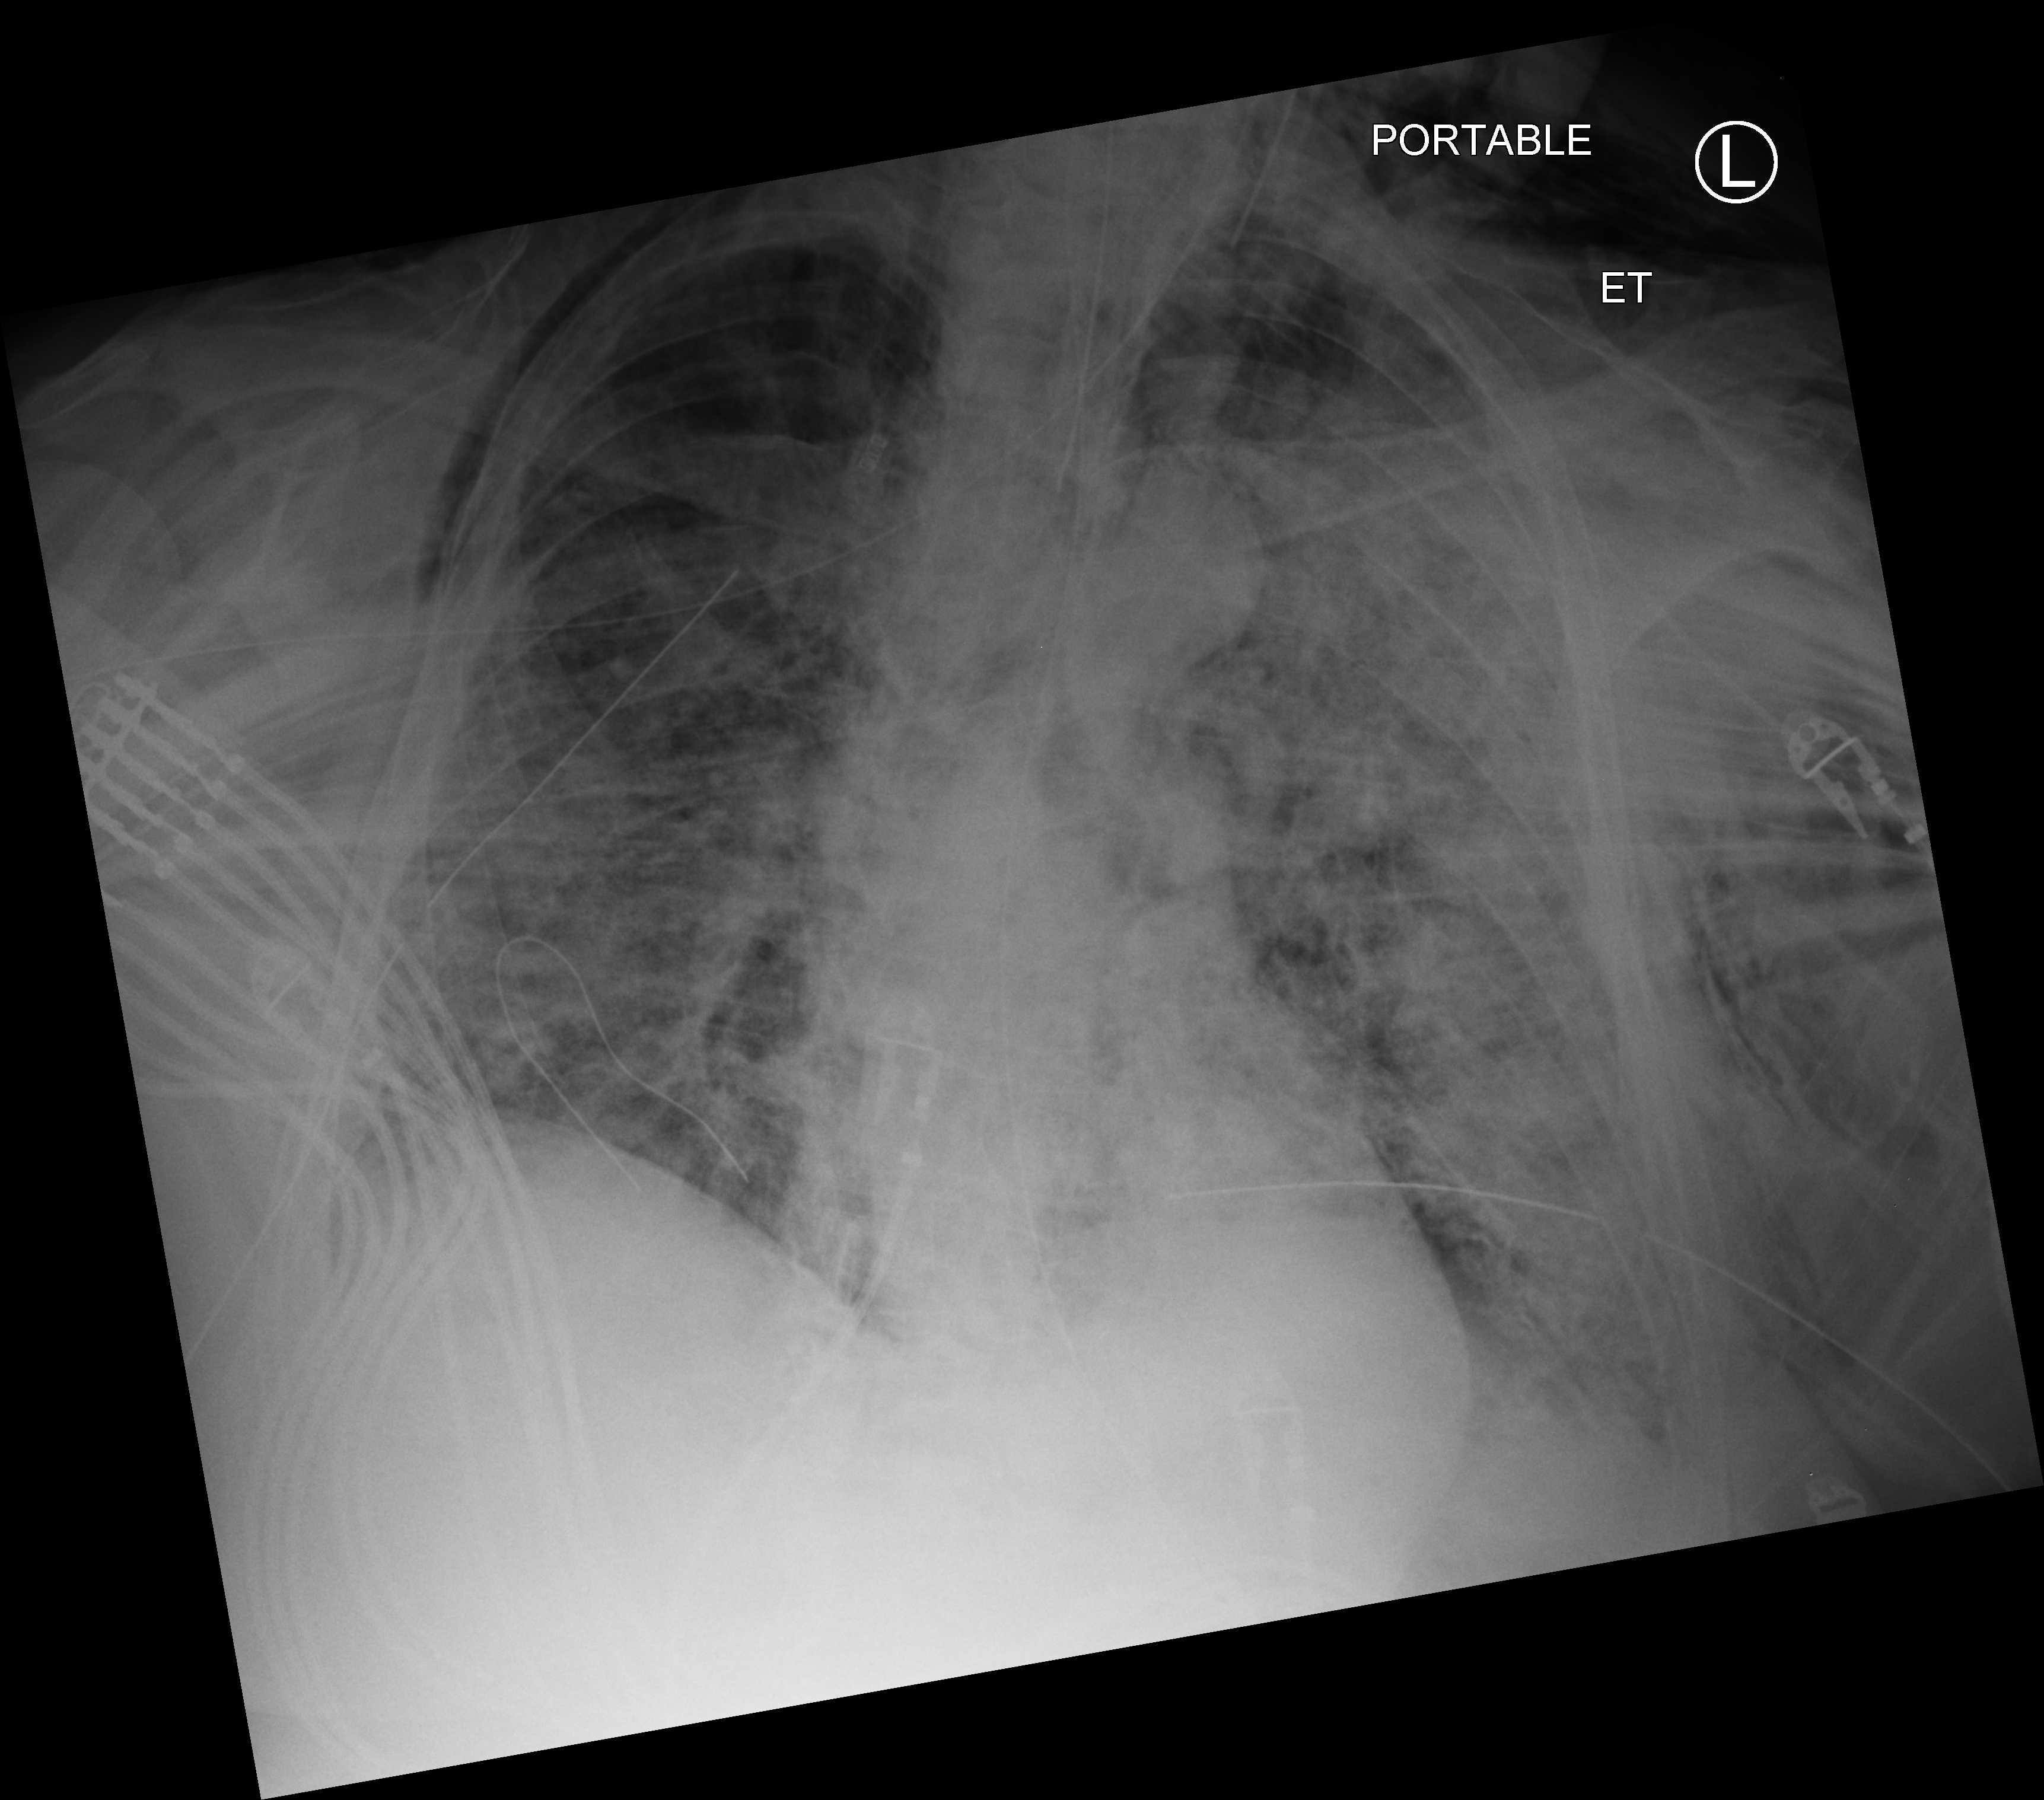
Chest X-ray (portable), anteroposterior (AP) projection. Adult patient hospitalised with COVID-19, age 18–59 years.
Hospital-stay facts (about this admission, not read from this image; timing relative to this image not recorded):
- admitted to intensive care during this hospital stay: yes
- length of hospital stay: 28 days
- mechanically ventilated during this hospital stay: yes